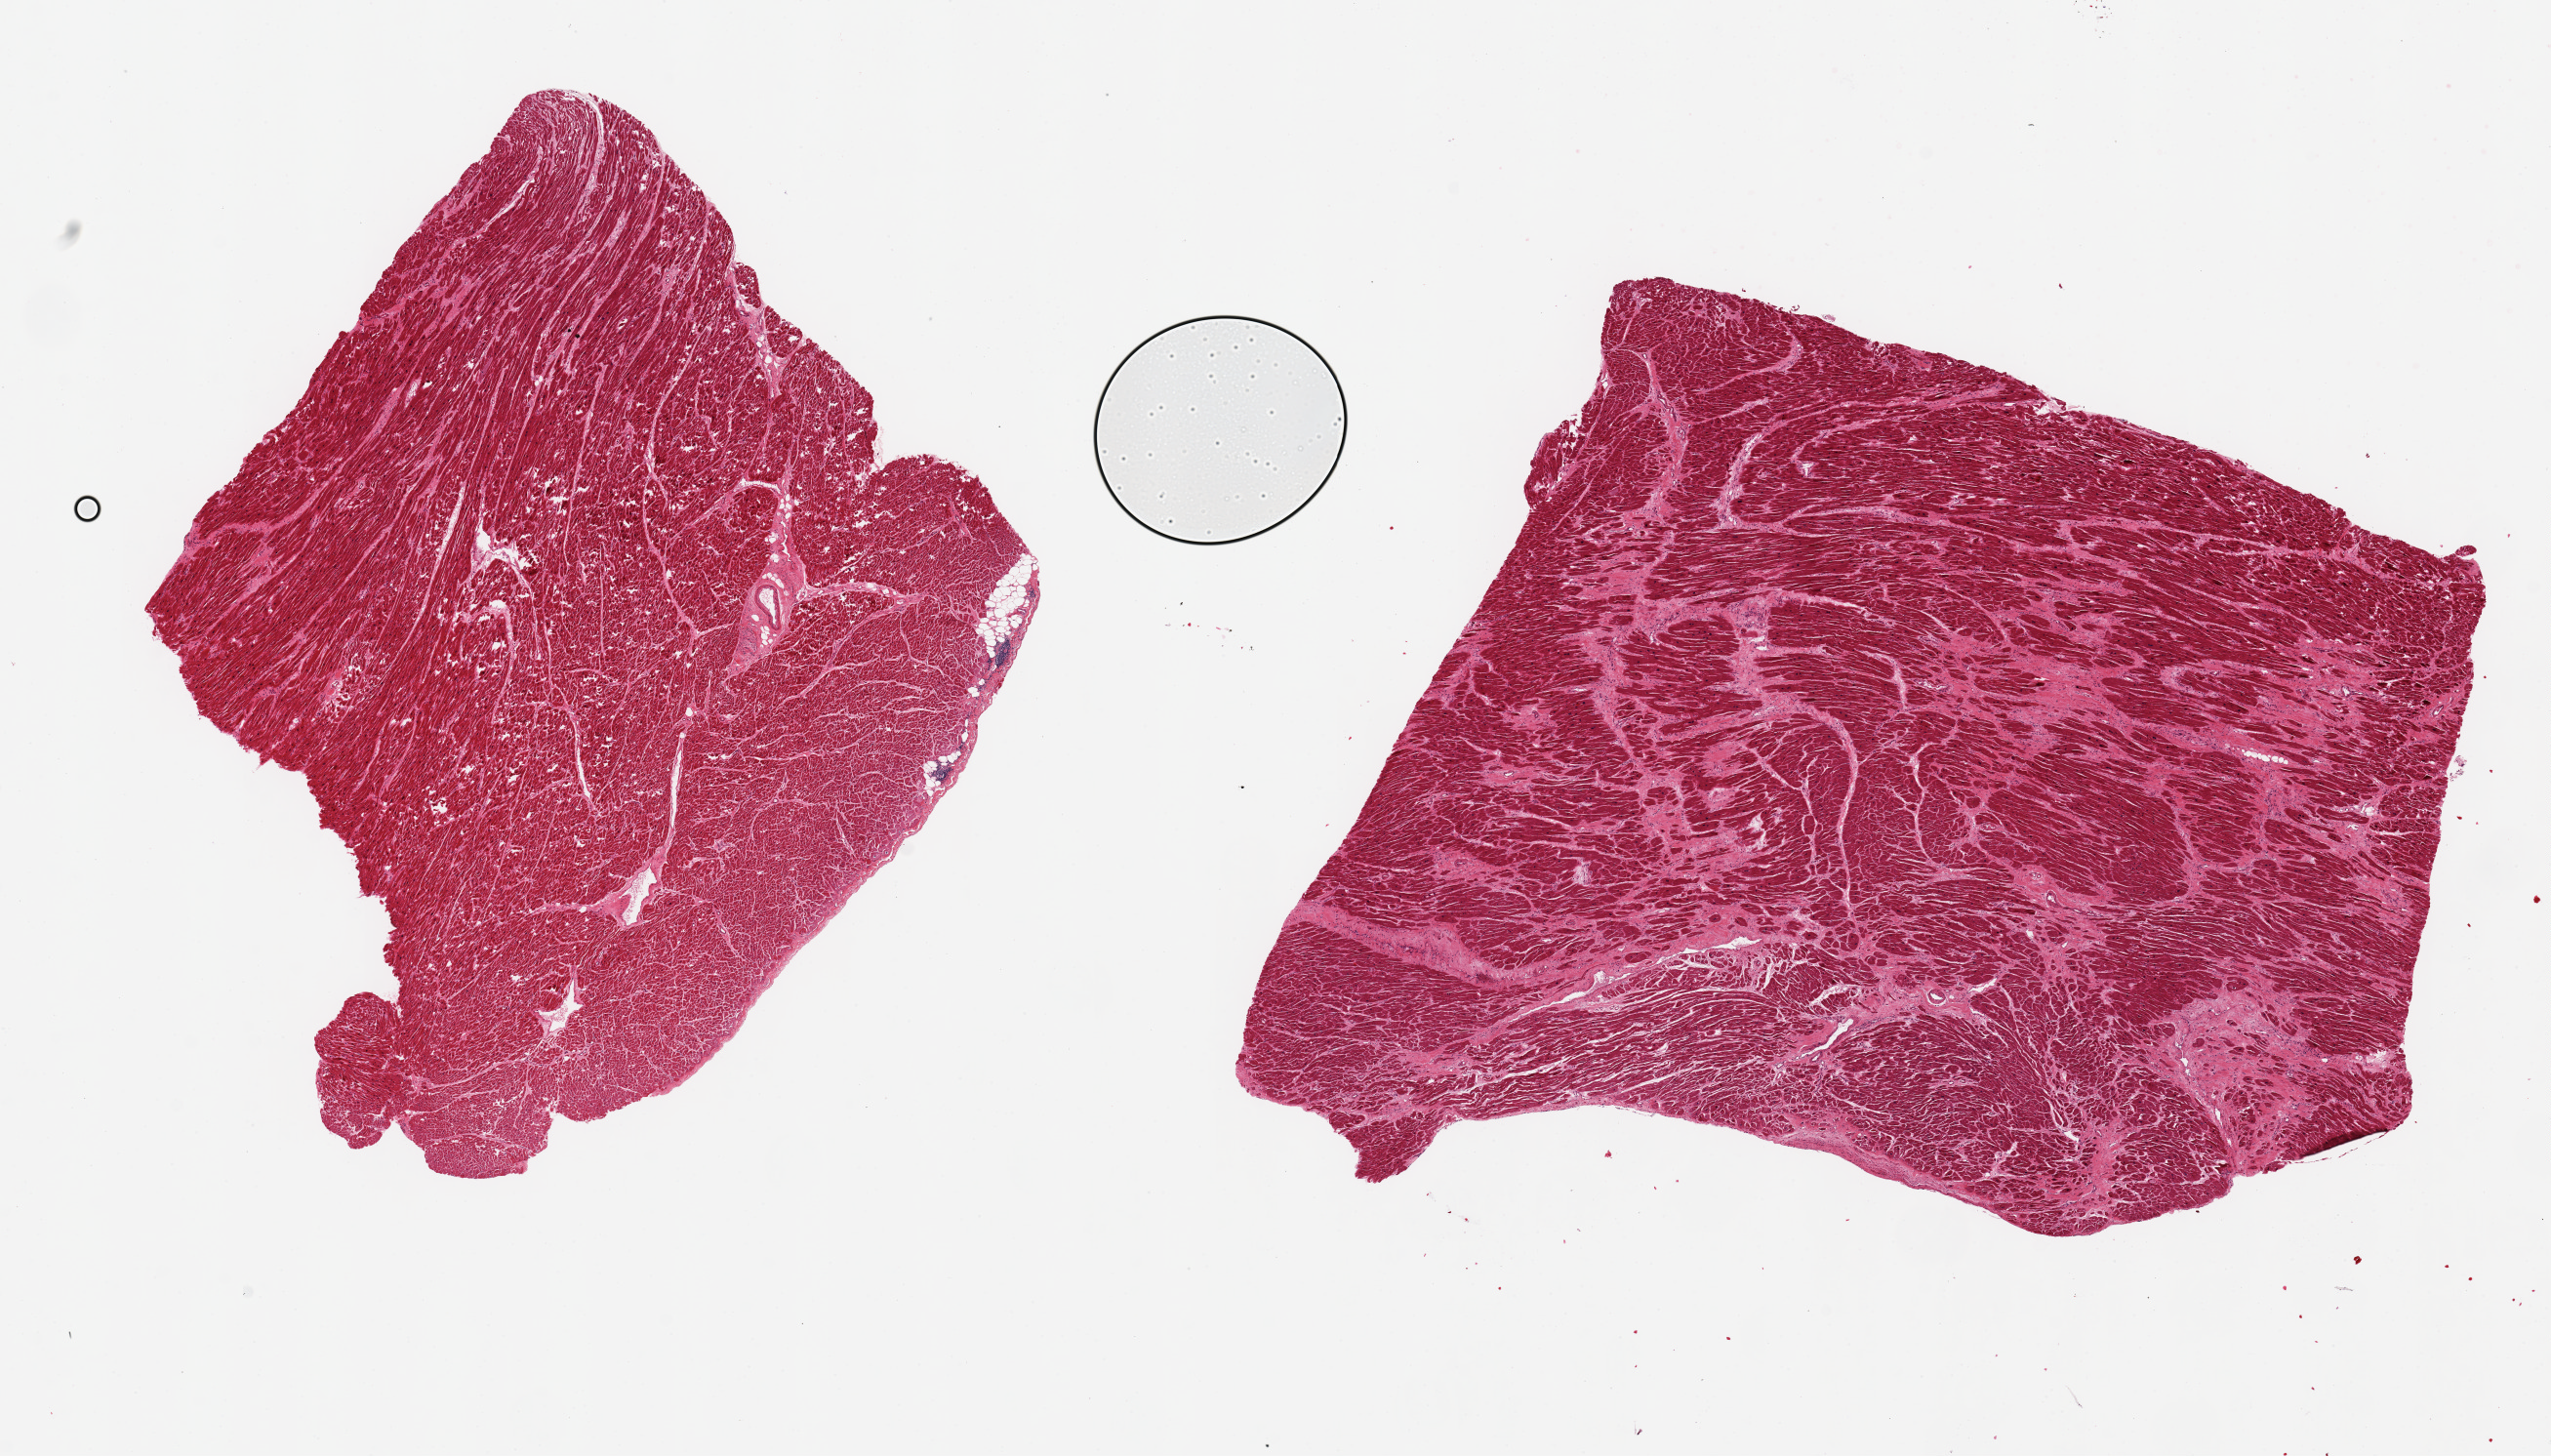
Hematoxylin and eosin (H&E) whole-slide image, shown as a low-resolution overview of the whole scanned area (about 20.7 x 11.8 mm, acquisition: 20x scan); PAXgene-fixed, paraffin-embedded tissue; section of heart (target tissue); donor tissue sample. Donor sex: male.
Reviewer comment on this tissue sample: 2 pieces~7x6mm patchy moderate interstitial fibrosis/infacrcts.